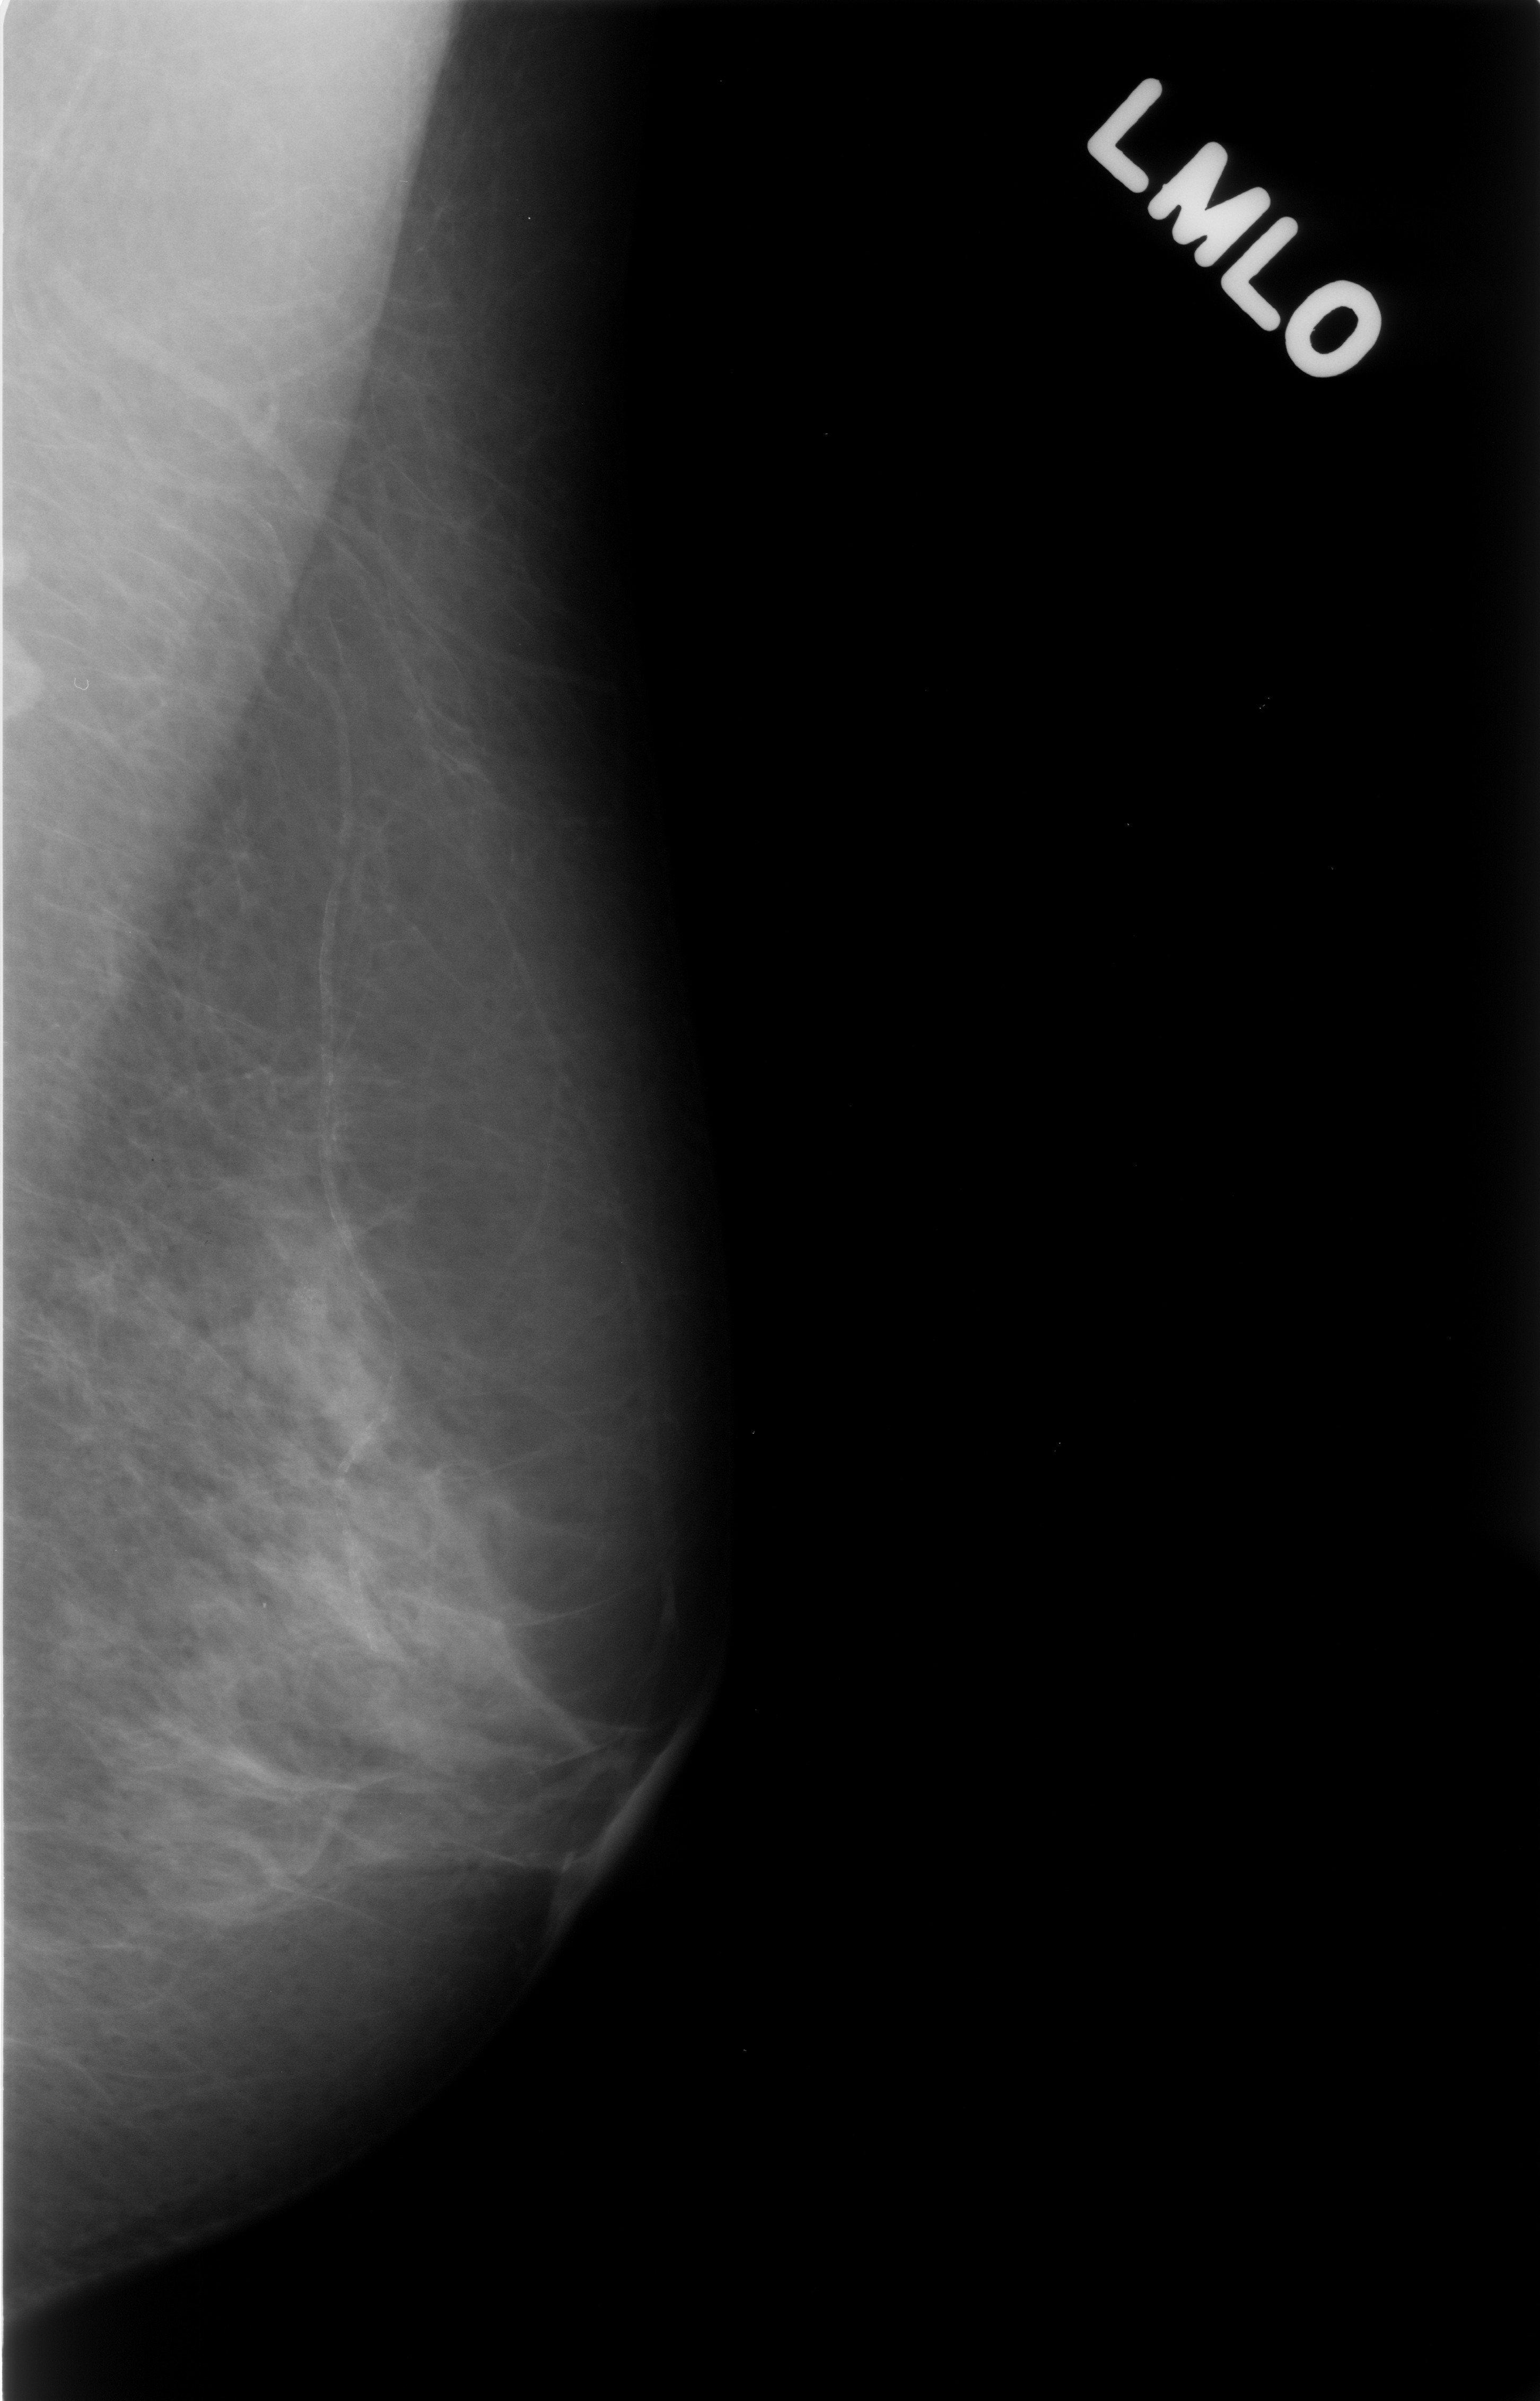
Mammogram (digitized film); left breast; MLO view; BI-RADS breast density category 2 (scale 1–4).
Marked findings (only marked abnormalities are described; nothing is implied about the rest of the image): calcifications, morphology amorphous, distribution clustered; BI-RADS assessment category 4; subtlety rating 2 on a 1 (subtle) to 5 (obvious) scale; pathology result (as recorded, not read from the image): benign.